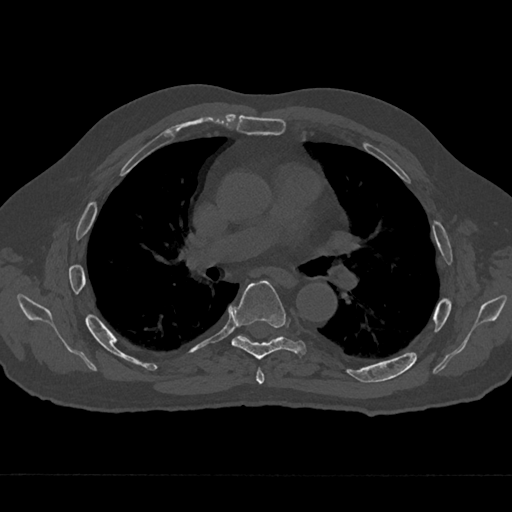
CT including the spine, one axial slice; position 420 of 797 along the scan axis; reconstruction kernel Br40s/3; bone window (W 1800 / L 400 HU); 0.5 mm slice thickness; 512 × 512 image matrix. Male patient, age 75 years. From the clinical record (not read from this slice): primary cancer: renal; vertebrae with lytic lesions (as recorded): T4.
Structures marked on this image (semi-automatically segmented with operator editing):
- T5 vertebra: bounding box (x1, y1, x2, y2) in pixels: (256, 368, 265, 385)
- T6 vertebra: (231, 280, 307, 359)